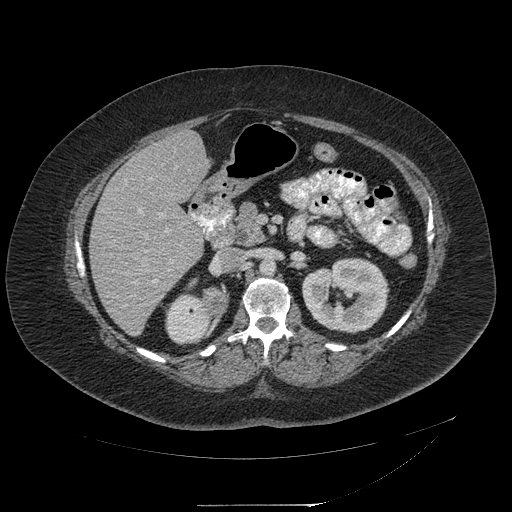
Contrast-enhanced abdominal CT, one axial slice; slice 110 of 217 in the series (ordered by position); intravenous contrast given; soft-tissue window (W 400 / L 40 HU); 1.25 mm slice thickness; 512 × 512 image matrix, field of view 453 × 453 mm. Patient: female, 55 years. From the clinical record (not read from this slice): diagnosis: adrenocortical carcinoma; tumour side: right adrenal; tumour size at pathology: 11 cm; Ki-67 index: 20 %; stage (as recorded): 2.
Structures marked on this image (semi-automatic segmentation, software-assisted and operator-edited):
- mass: box from (x=205, y=289) to (x=228, y=315) px